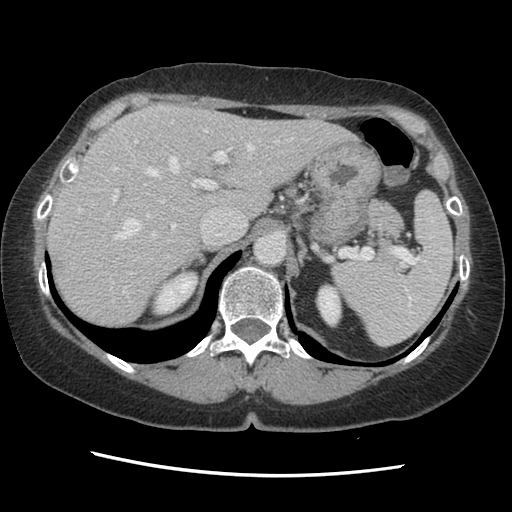
Contrast-enhanced abdominal CT, one axial slice; position 97 of 141 along the scan axis; soft-tissue window (W 400 / L 40 HU); 512 × 512 image matrix. Female patient, age 61 years. Case-level facts recorded for this patient, not image findings: diagnosis: colorectal cancer liver metastases, imaged before liver resection; multiple liver metastases: no; largest metastasis: 2.4 cm.
Structures marked on this image (outlined manually by an expert reader):
- hepatic veins: bounding box (x1, y1, x2, y2) in pixels: (77, 120, 294, 295)
- liver: (48, 105, 350, 328)
- planned liver remnant (the part of the liver to remain after resection): (48, 105, 350, 328)
- portal vein (with intrahepatic branches): (112, 139, 231, 232)